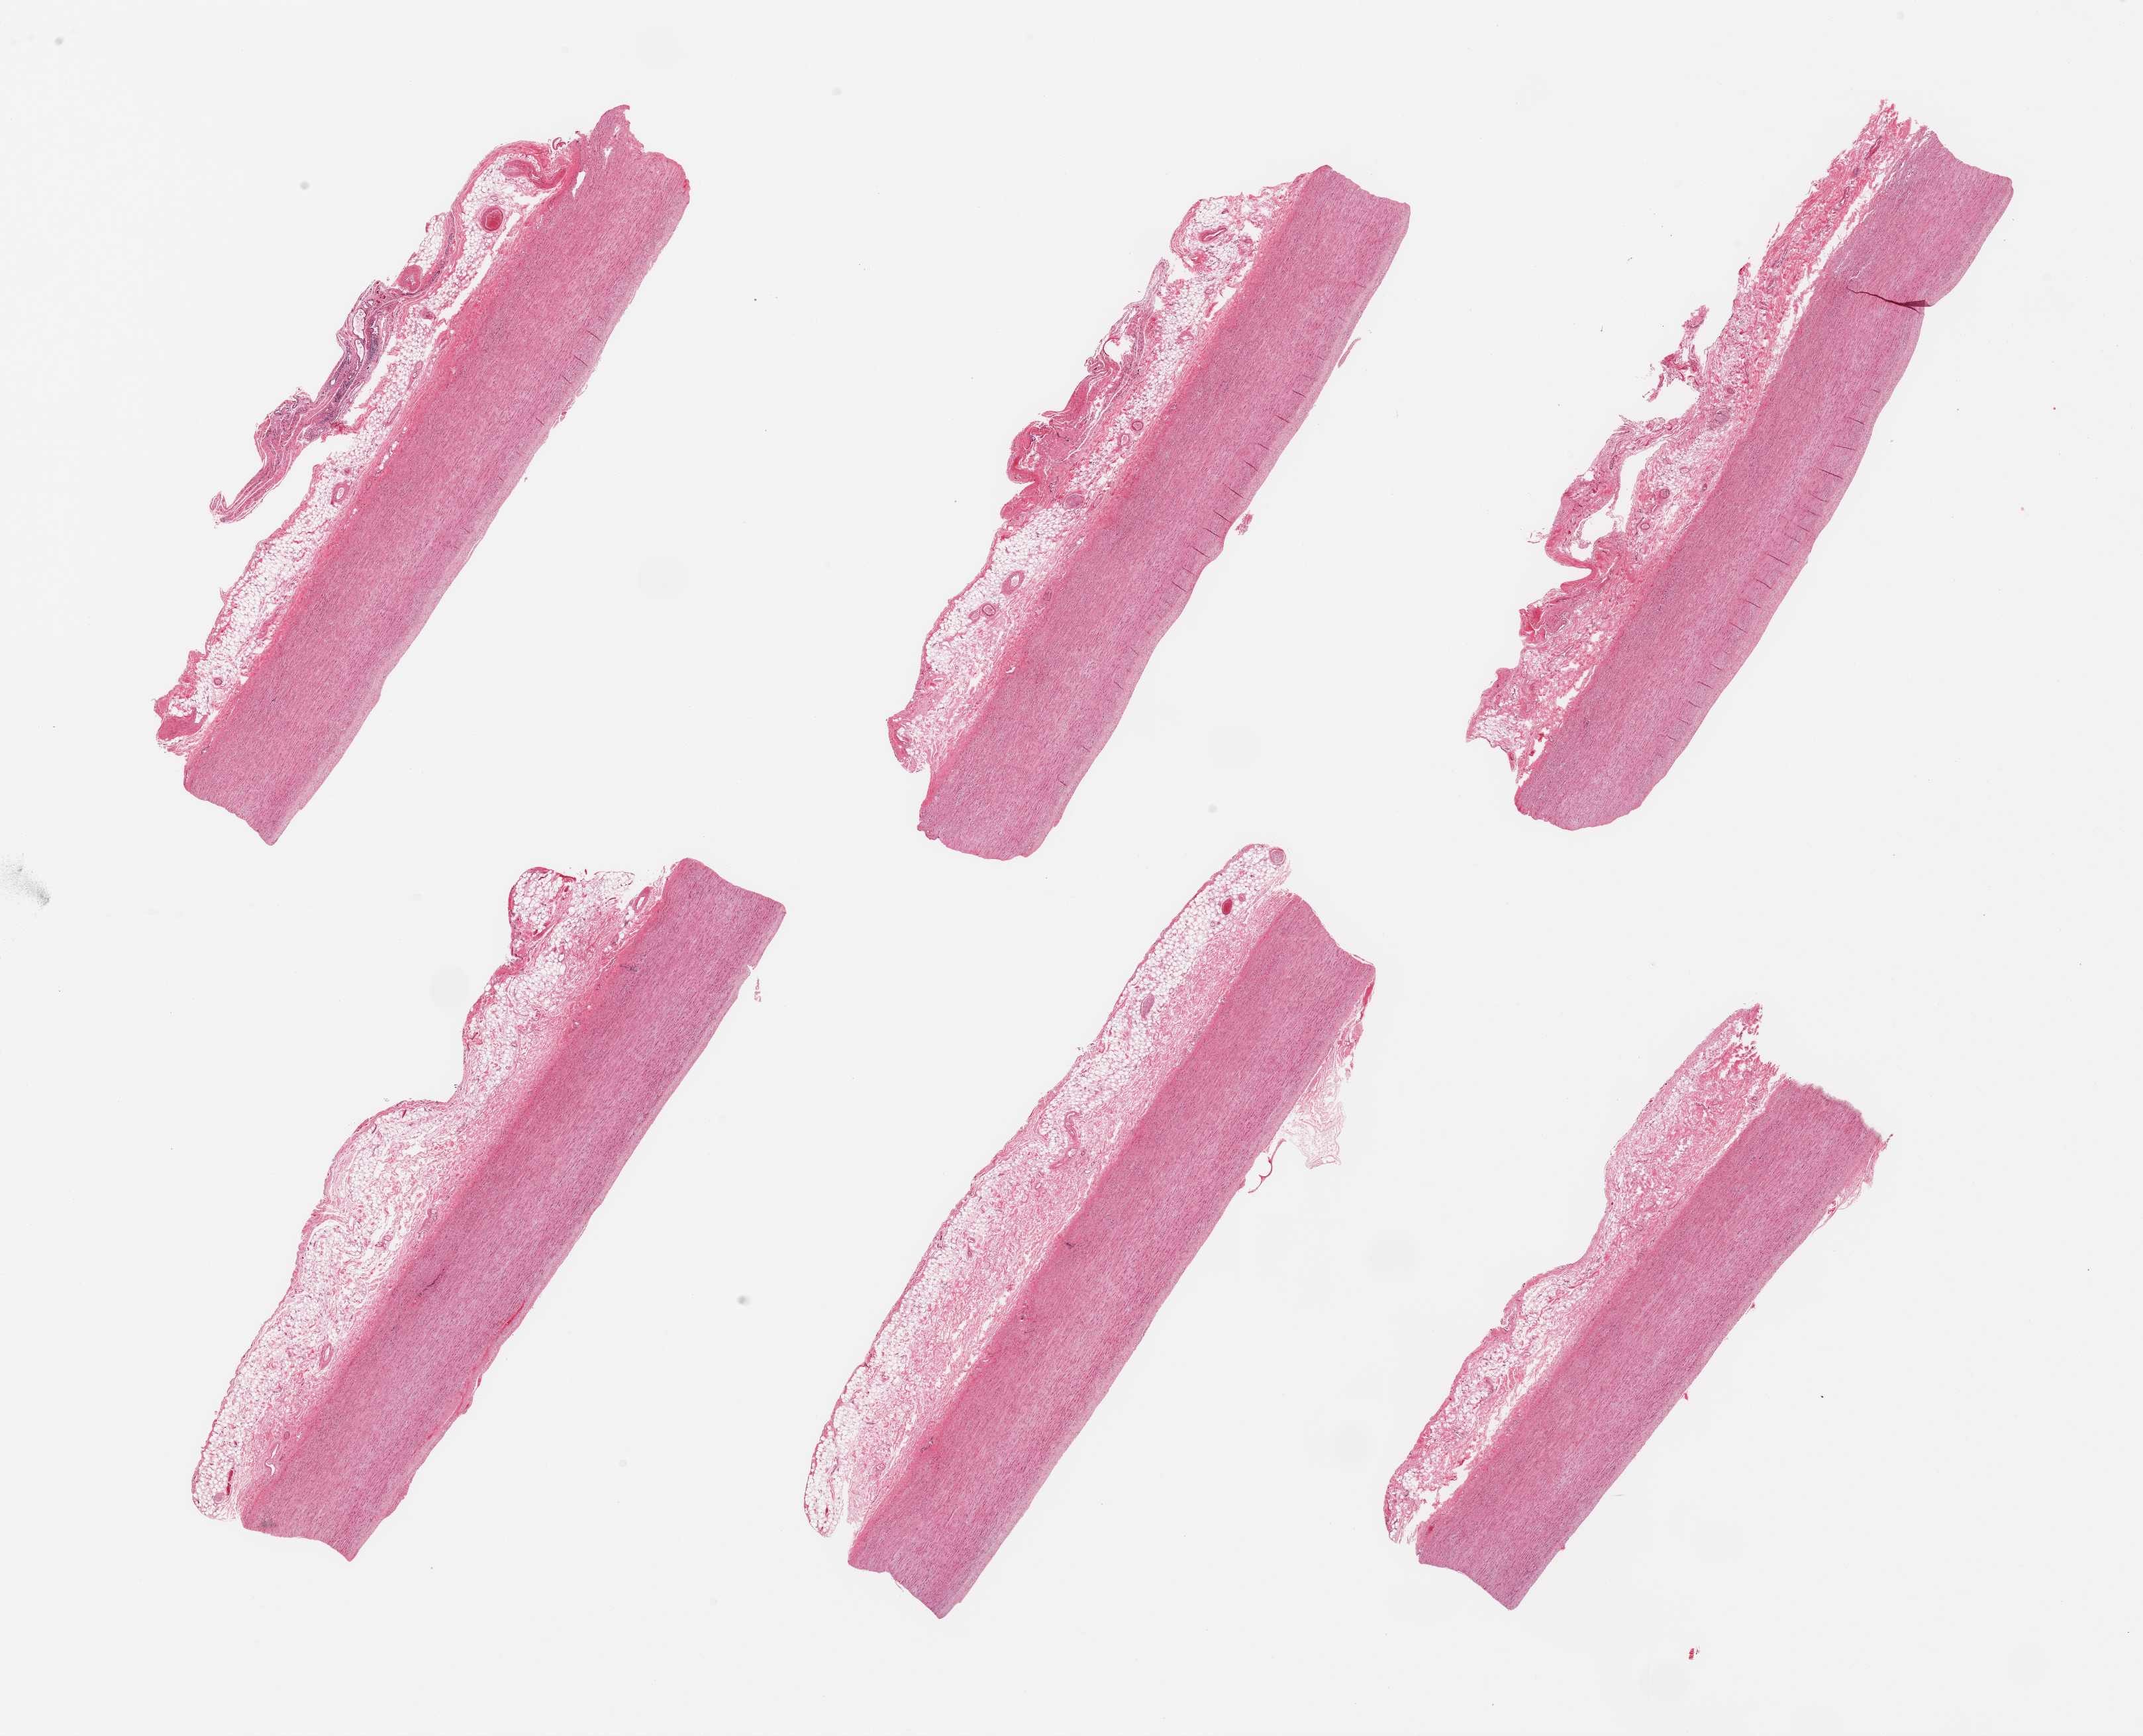
Digitized haematoxylin and eosin-stained section — shown as a low-resolution overview of the whole scanned area (about 25.6 x 20.7 mm, slide scanned at 20x). PAXgene-fixed, paraffin-embedded tissue. Target tissue: aorta. Donor tissue sample. Male donor.
Pathologist's review note for this sample: 6 pieces; minimal plaque; 1mm thick fibrous adventitia.